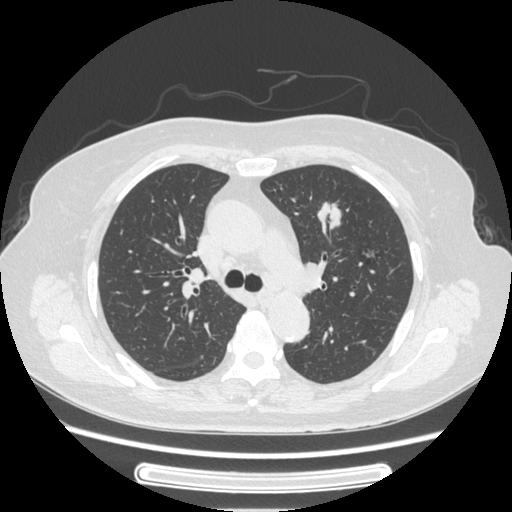
Chest CT, one axial slice; position 161 of 227 along the scan axis; lung window (W 1500 / L -600 HU); 1.25 mm slice thickness; 512 × 512 image matrix, field of view 363 × 363 mm. Patient: female, 77 years. From the clinical record (not read from this slice): clinical TNM (as recorded): T1c N3 M0.
Annotated regions visible in this slice (bounding box drawn by a radiologist):
- lung tumour (recorded histology: adenocarcinoma): bounding box [x1, y1, x2, y2] px = [317, 192, 344, 240]